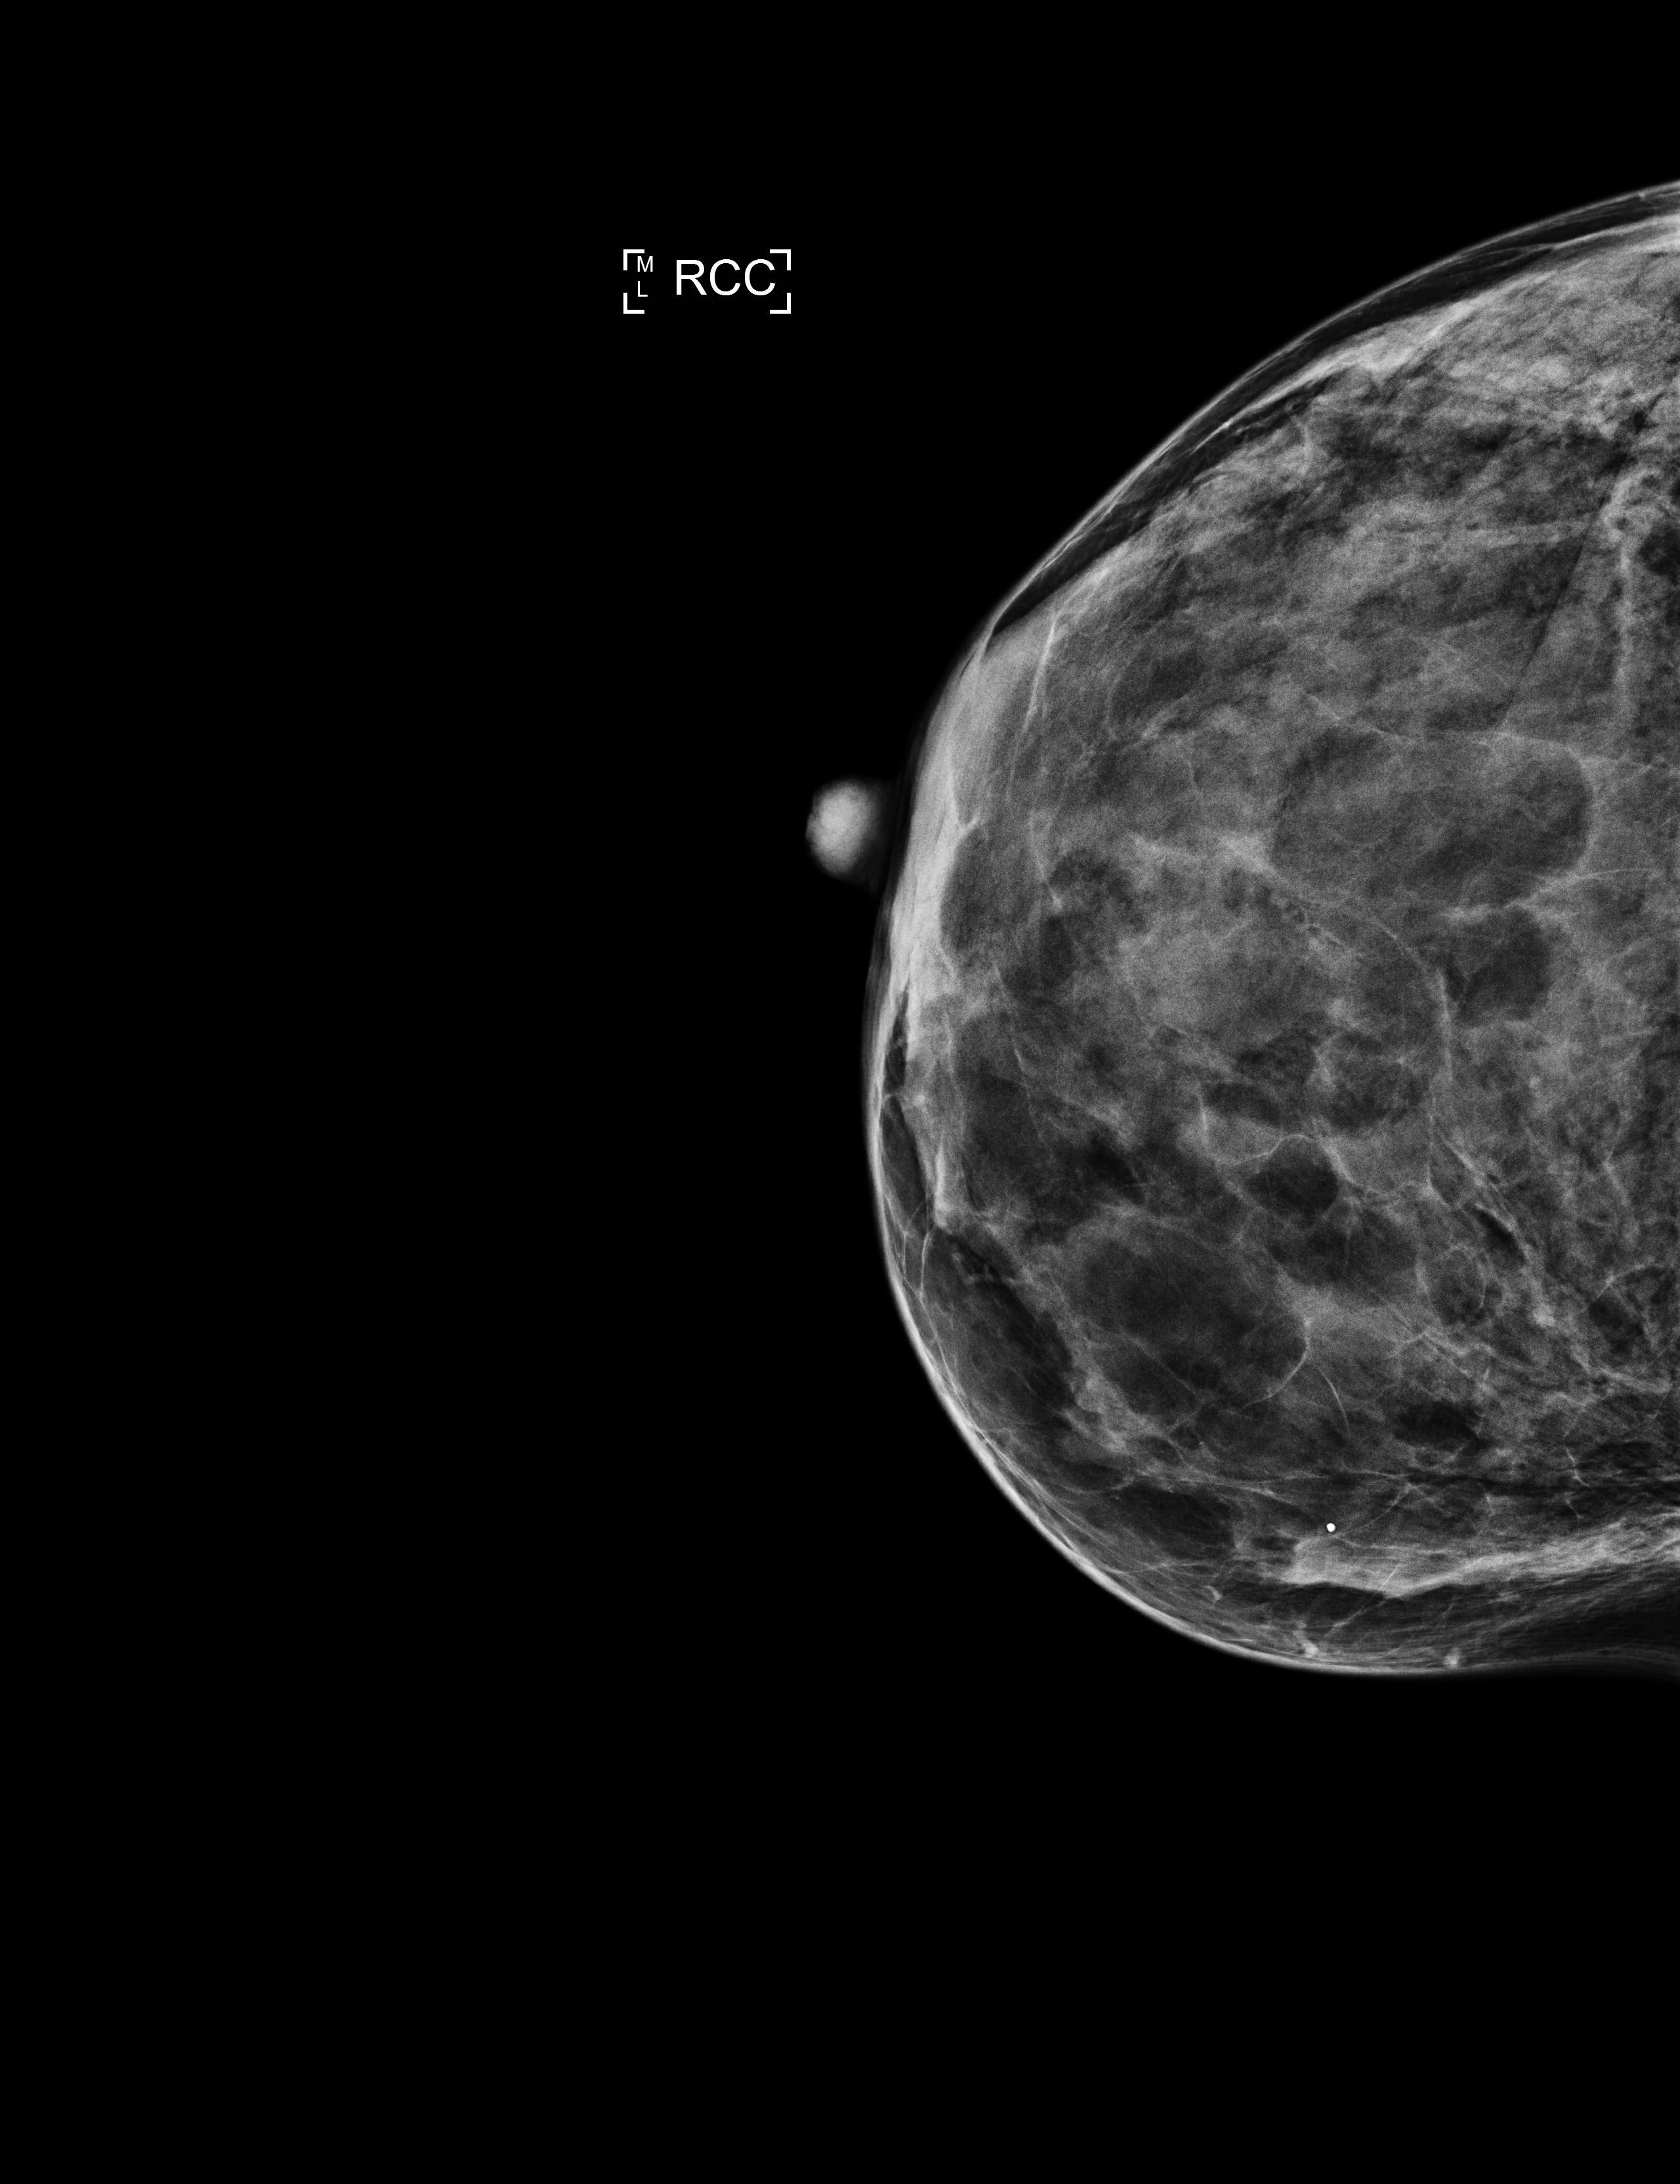
Screening examination; compressed breast thickness 32 mm; system: Selenia Dimensions. Patient: female, 56 years.
Image type: full-field digital mammogram. Breast: right. Projection: cranio-caudal projection.